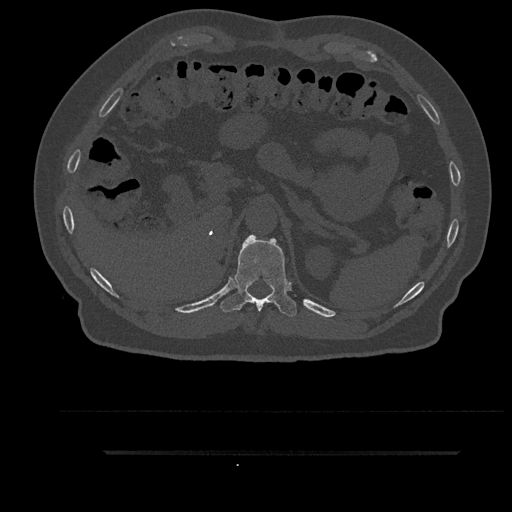
CT including the spine, one axial slice; position 309 of 797 along the scan axis; reconstruction kernel Br40s/3; 120 kVp; bone window (W 1800 / L 400 HU); 0.5 mm slice thickness; 512 × 512 image matrix, field of view 432 × 432 mm. Patient: male, 63 years. Case-level facts recorded for this patient, not image findings: primary cancer: renal; vertebrae with lytic lesions (as recorded): T8.
Annotated regions visible in this slice (semi-automatically segmented with operator editing):
- T11 vertebra: bounding box (x1, y1, x2, y2) in pixels: (221, 235, 297, 317)